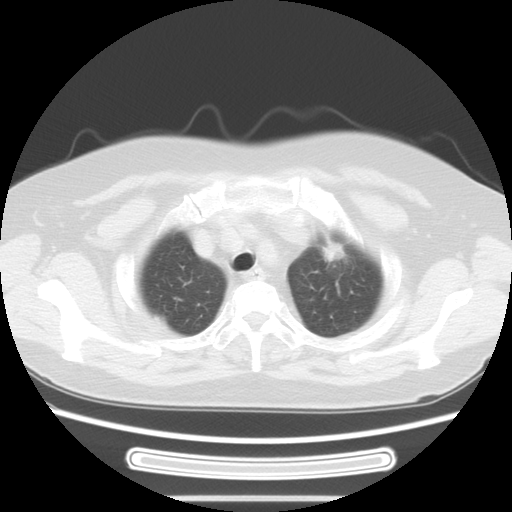
Chest CT, one axial slice. Position 49 of 58 along the scan axis. Lung window (W 1500 / L -600 HU). 5 mm slice thickness. 512 × 512 image matrix, field of view 350 × 350 mm. Patient: female, 70 years. From the clinical record (not read from this slice): clinical TNM (as recorded): T1c N0 M0; histopathological grade: G2-3.
Structures marked on this image (rectangle marked by the reading radiologist):
- lung tumour (recorded histology: adenocarcinoma): bounding box [x1, y1, x2, y2] px = [314, 229, 353, 274]